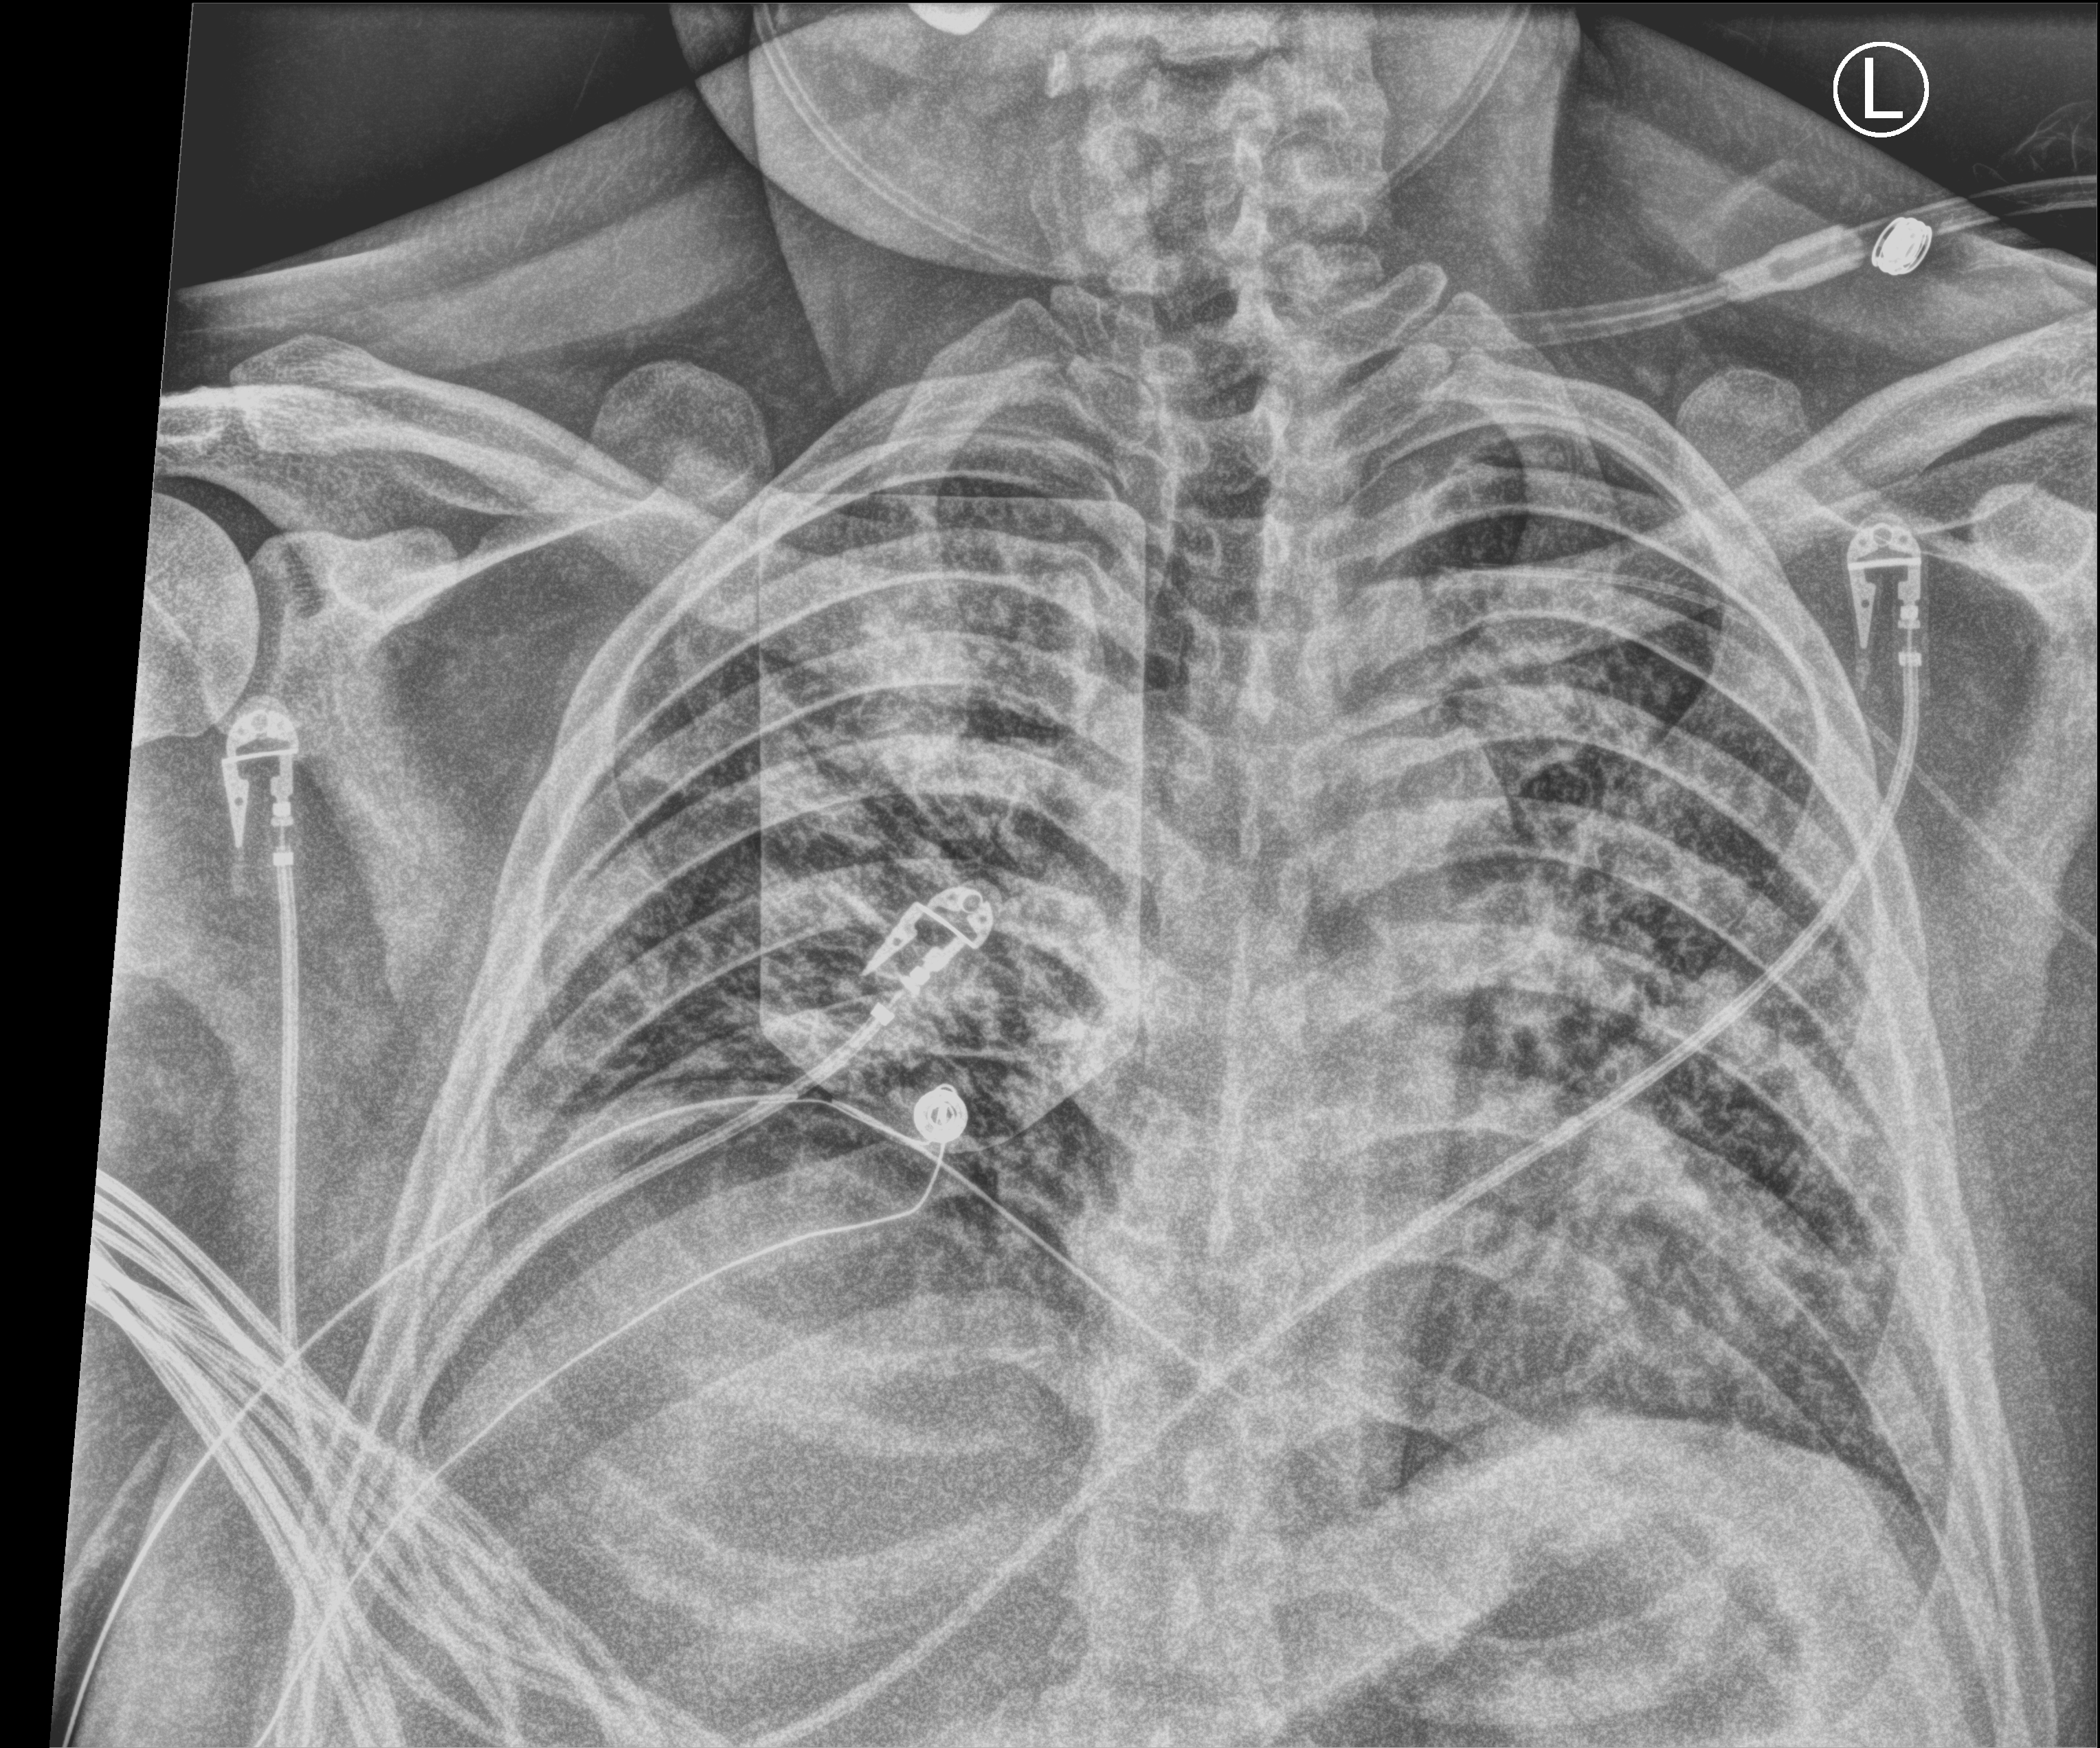
Portable chest radiograph, anteroposterior (AP) projection. Male patient hospitalised with COVID-19, age 18–59 years.
Admission-level facts for this patient (not findings on this image; timing relative to this image not recorded): mechanically ventilated during this hospital stay: yes.